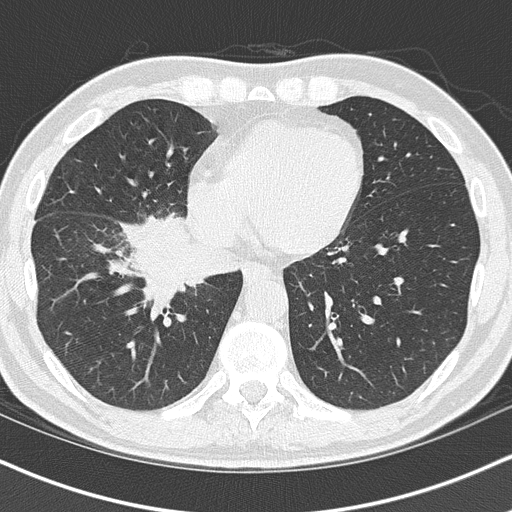
Low-dose screening chest CT, one axial slice. Slice 44 of 151 in the series (ordered by position). Lung window (W 1500 / L -600 HU). 512 × 512 image matrix, field of view 320 × 320 mm.
Annotated regions visible in this slice (expert manual segmentation):
- lesion 1 (tumor, hilum of right lung): bounding box [x1, y1, x2, y2] px = [123, 216, 192, 297]